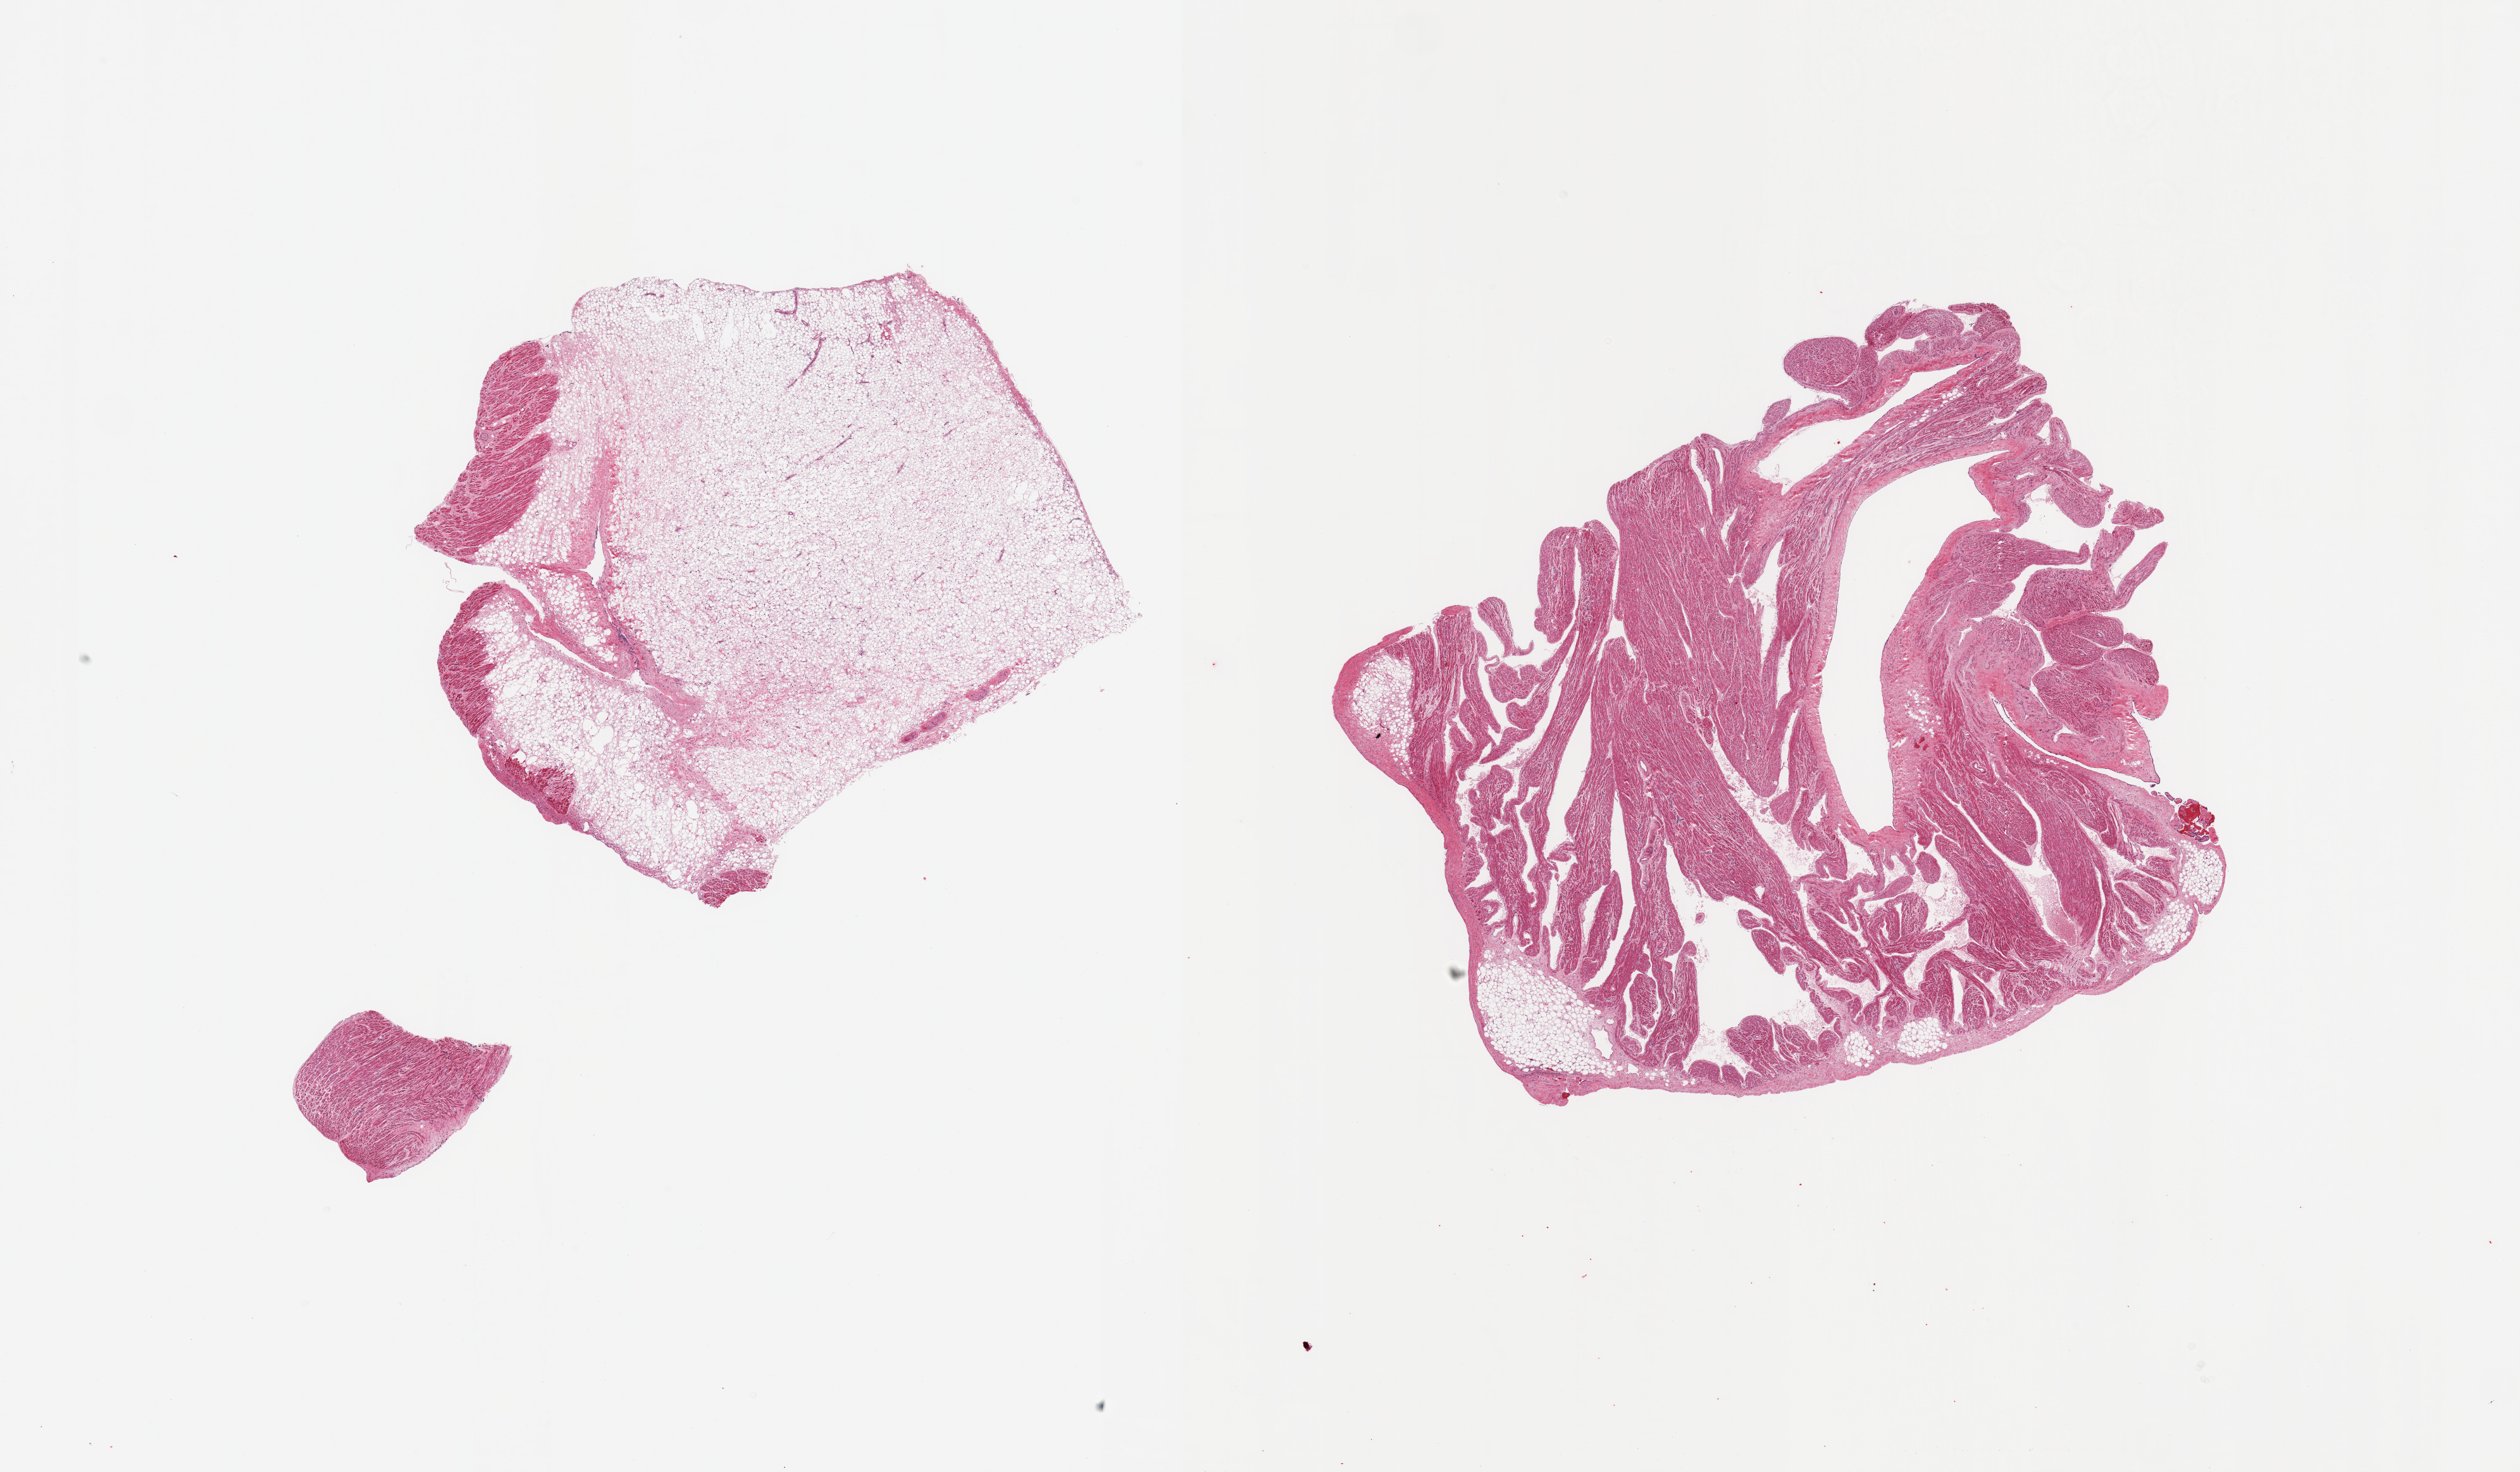
Digitized H&E-stained section — whole scanned area (about 31.5 x 18.4 mm, from a 20x scan) shown as a low-resolution overview; PAXgene-fixed paraffin-embedded (PFPE) section; section of auricular appendage (target tissue); tissue donor sample. Donor: male.
Pathologist's review note for this sample: 2 pieces; 1 piece contains 90% fat, other 5%.